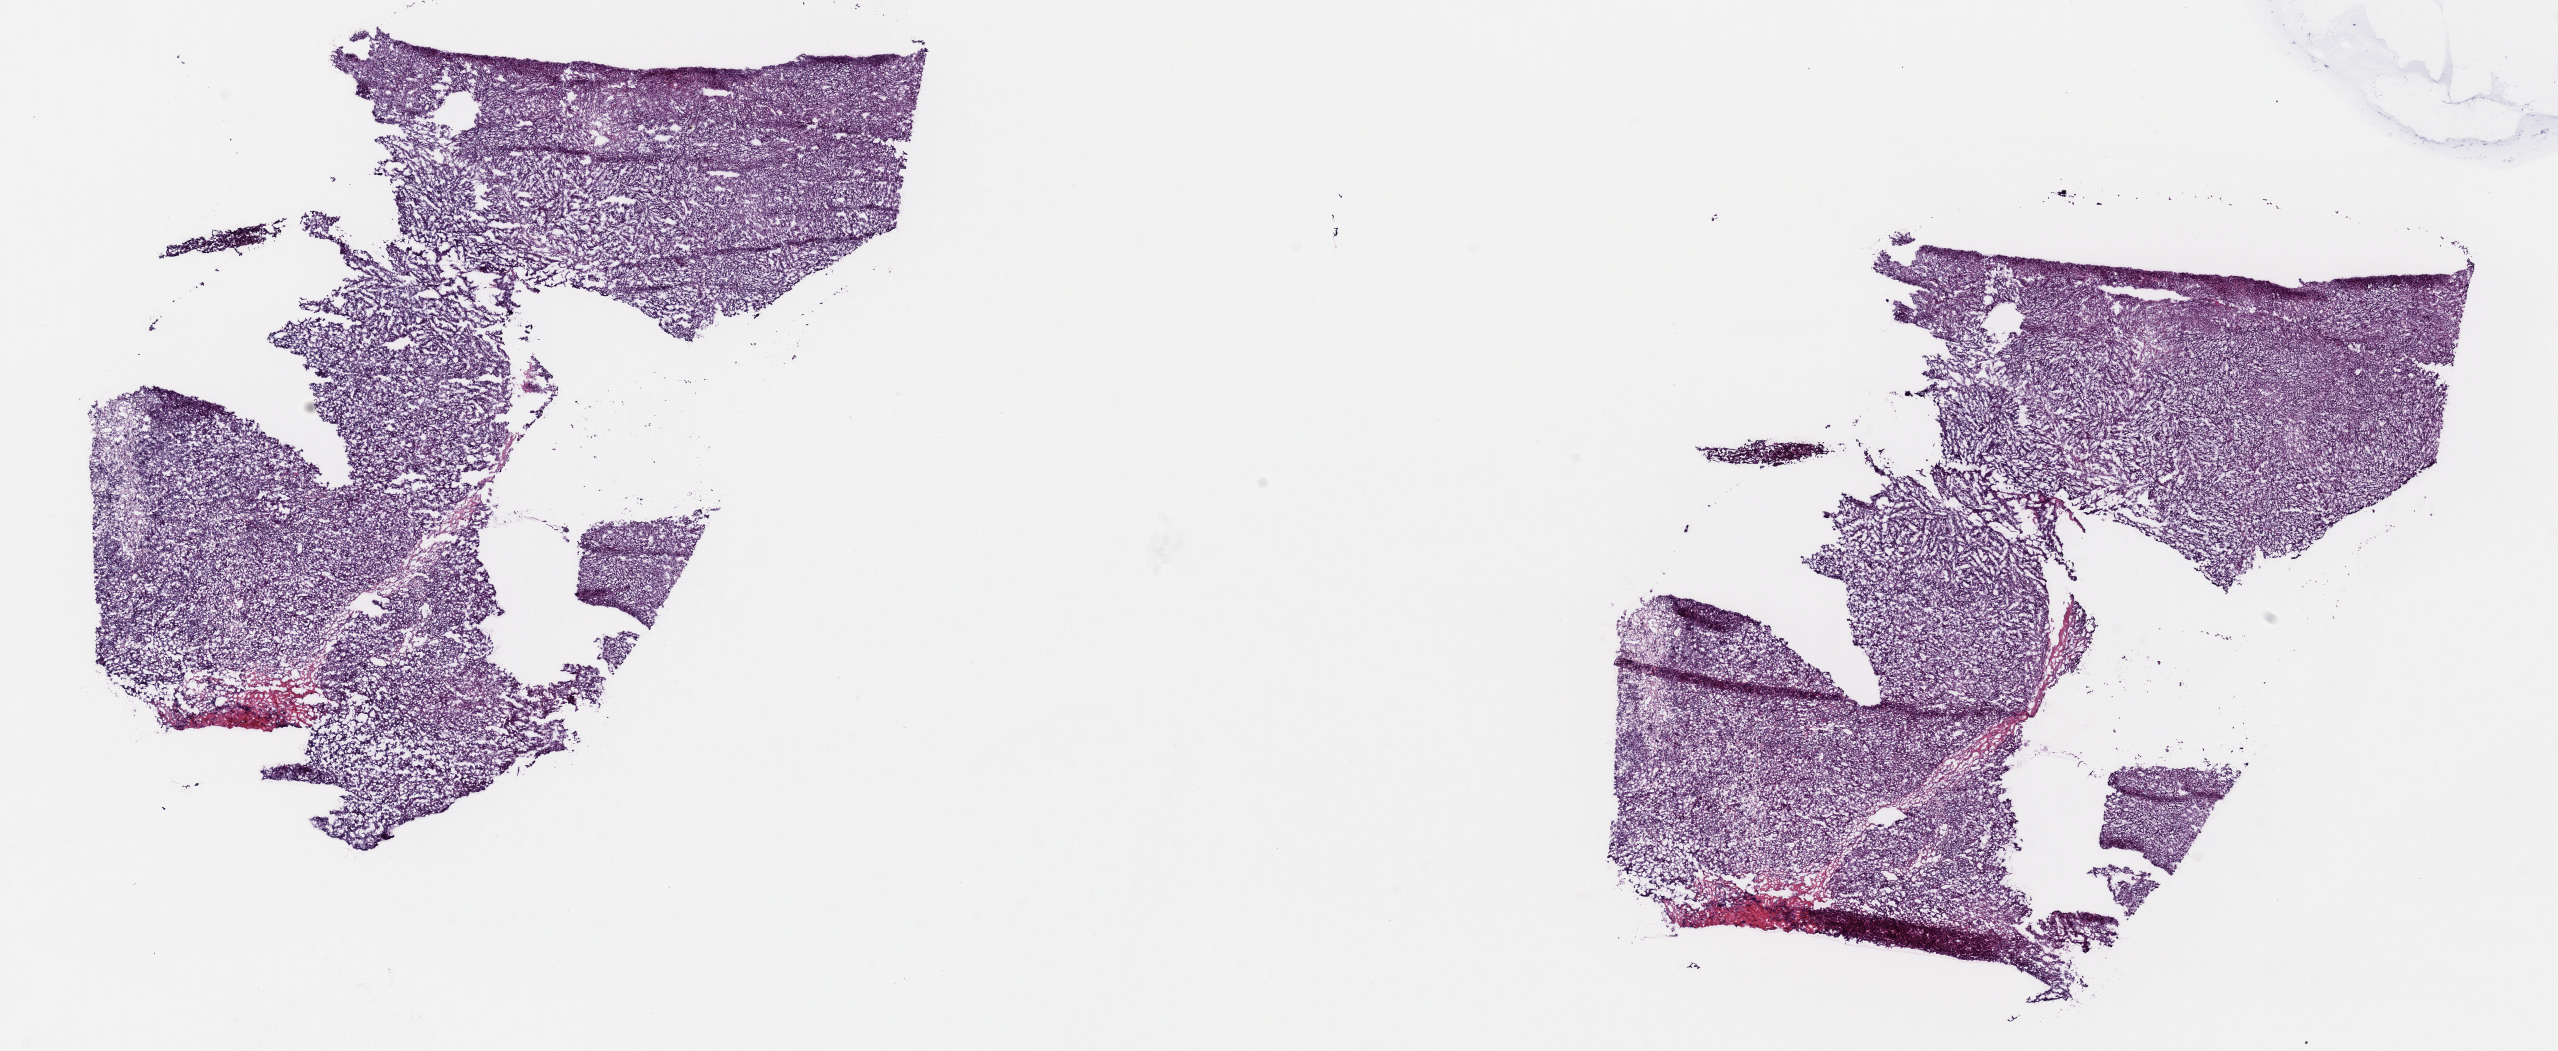
H&E whole-slide image, a low-resolution overview of the entire scanned area, about 20.2 x 8.3 mm (acquisition: 40x scan); frozen section from the top of the tissue portion; metastatic tumour sample, sampled site not recorded. Female patient; age at initial diagnosis 73 years.
This section: metastatic tumour tissue. Patient diagnosis: Malignant melanoma, NOS.